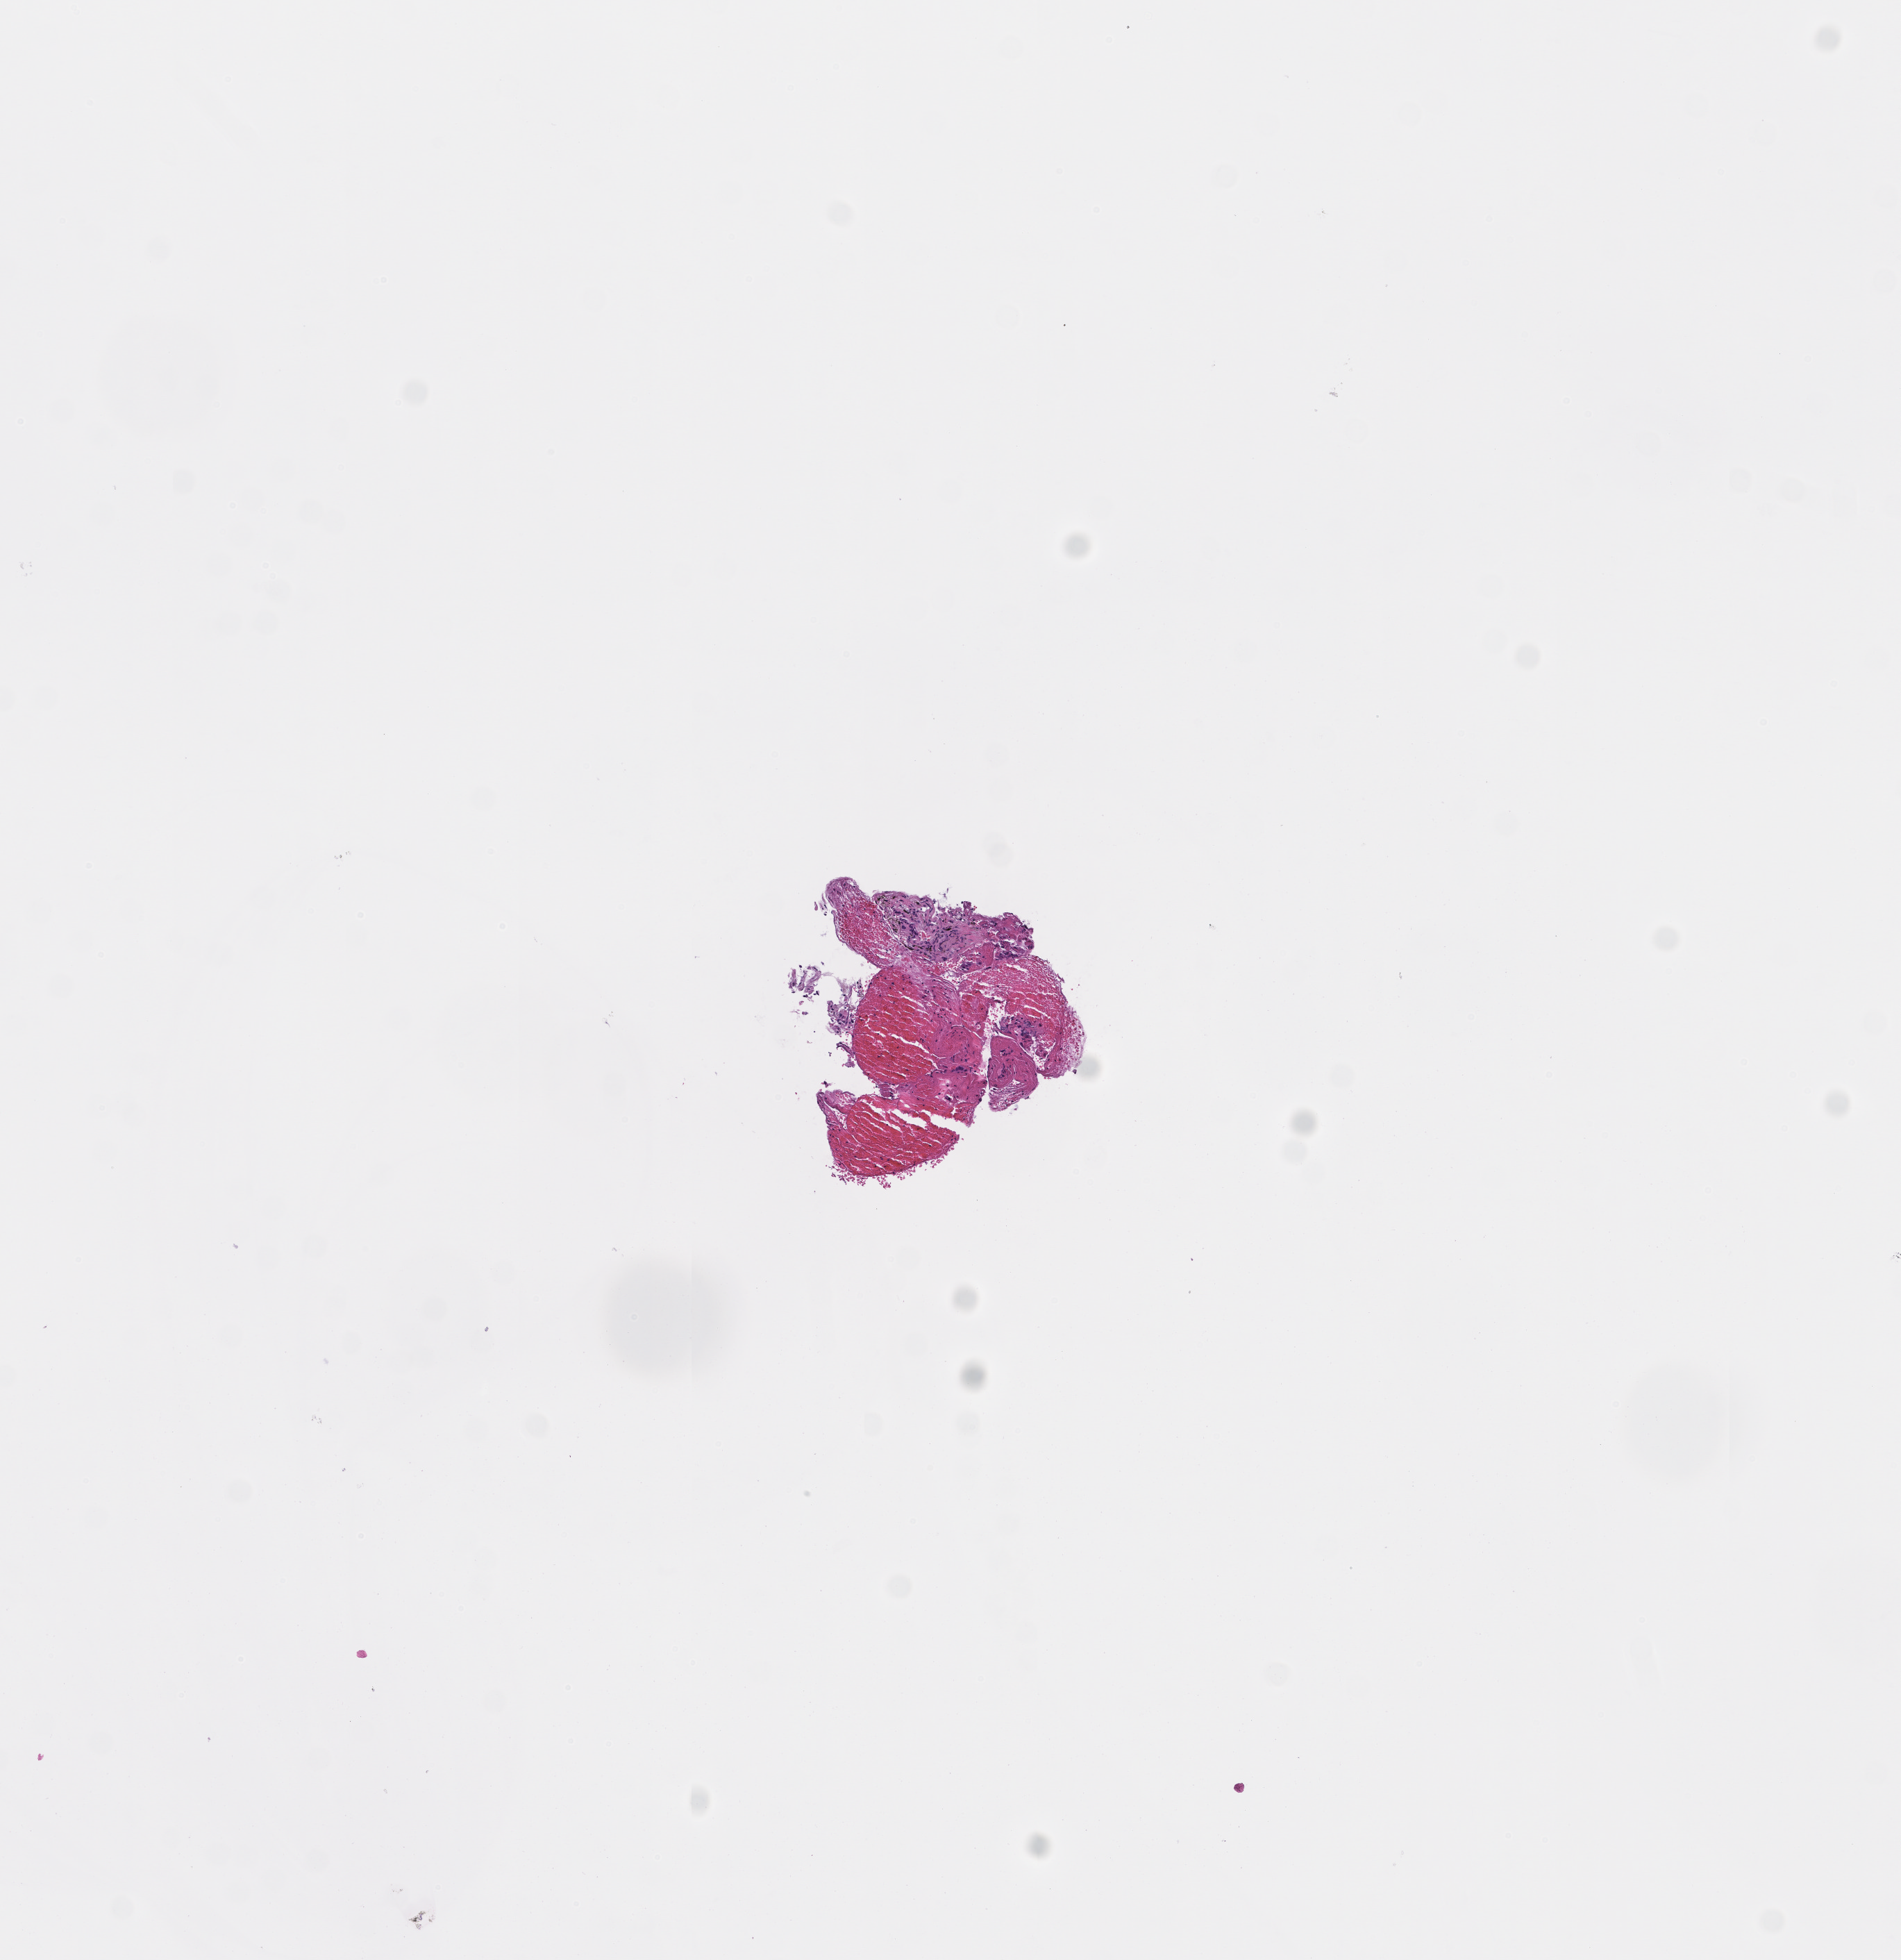
H&E whole-slide image — whole scanned area (about 5.5 x 5.7 mm) shown as a low-resolution overview; formalin-fixed paraffin-embedded section; site: lung; collected at disease progression. Patient sex: female.
This section: primary tumor. Diagnosis: Non-Small Cell Lung Carcinoma.